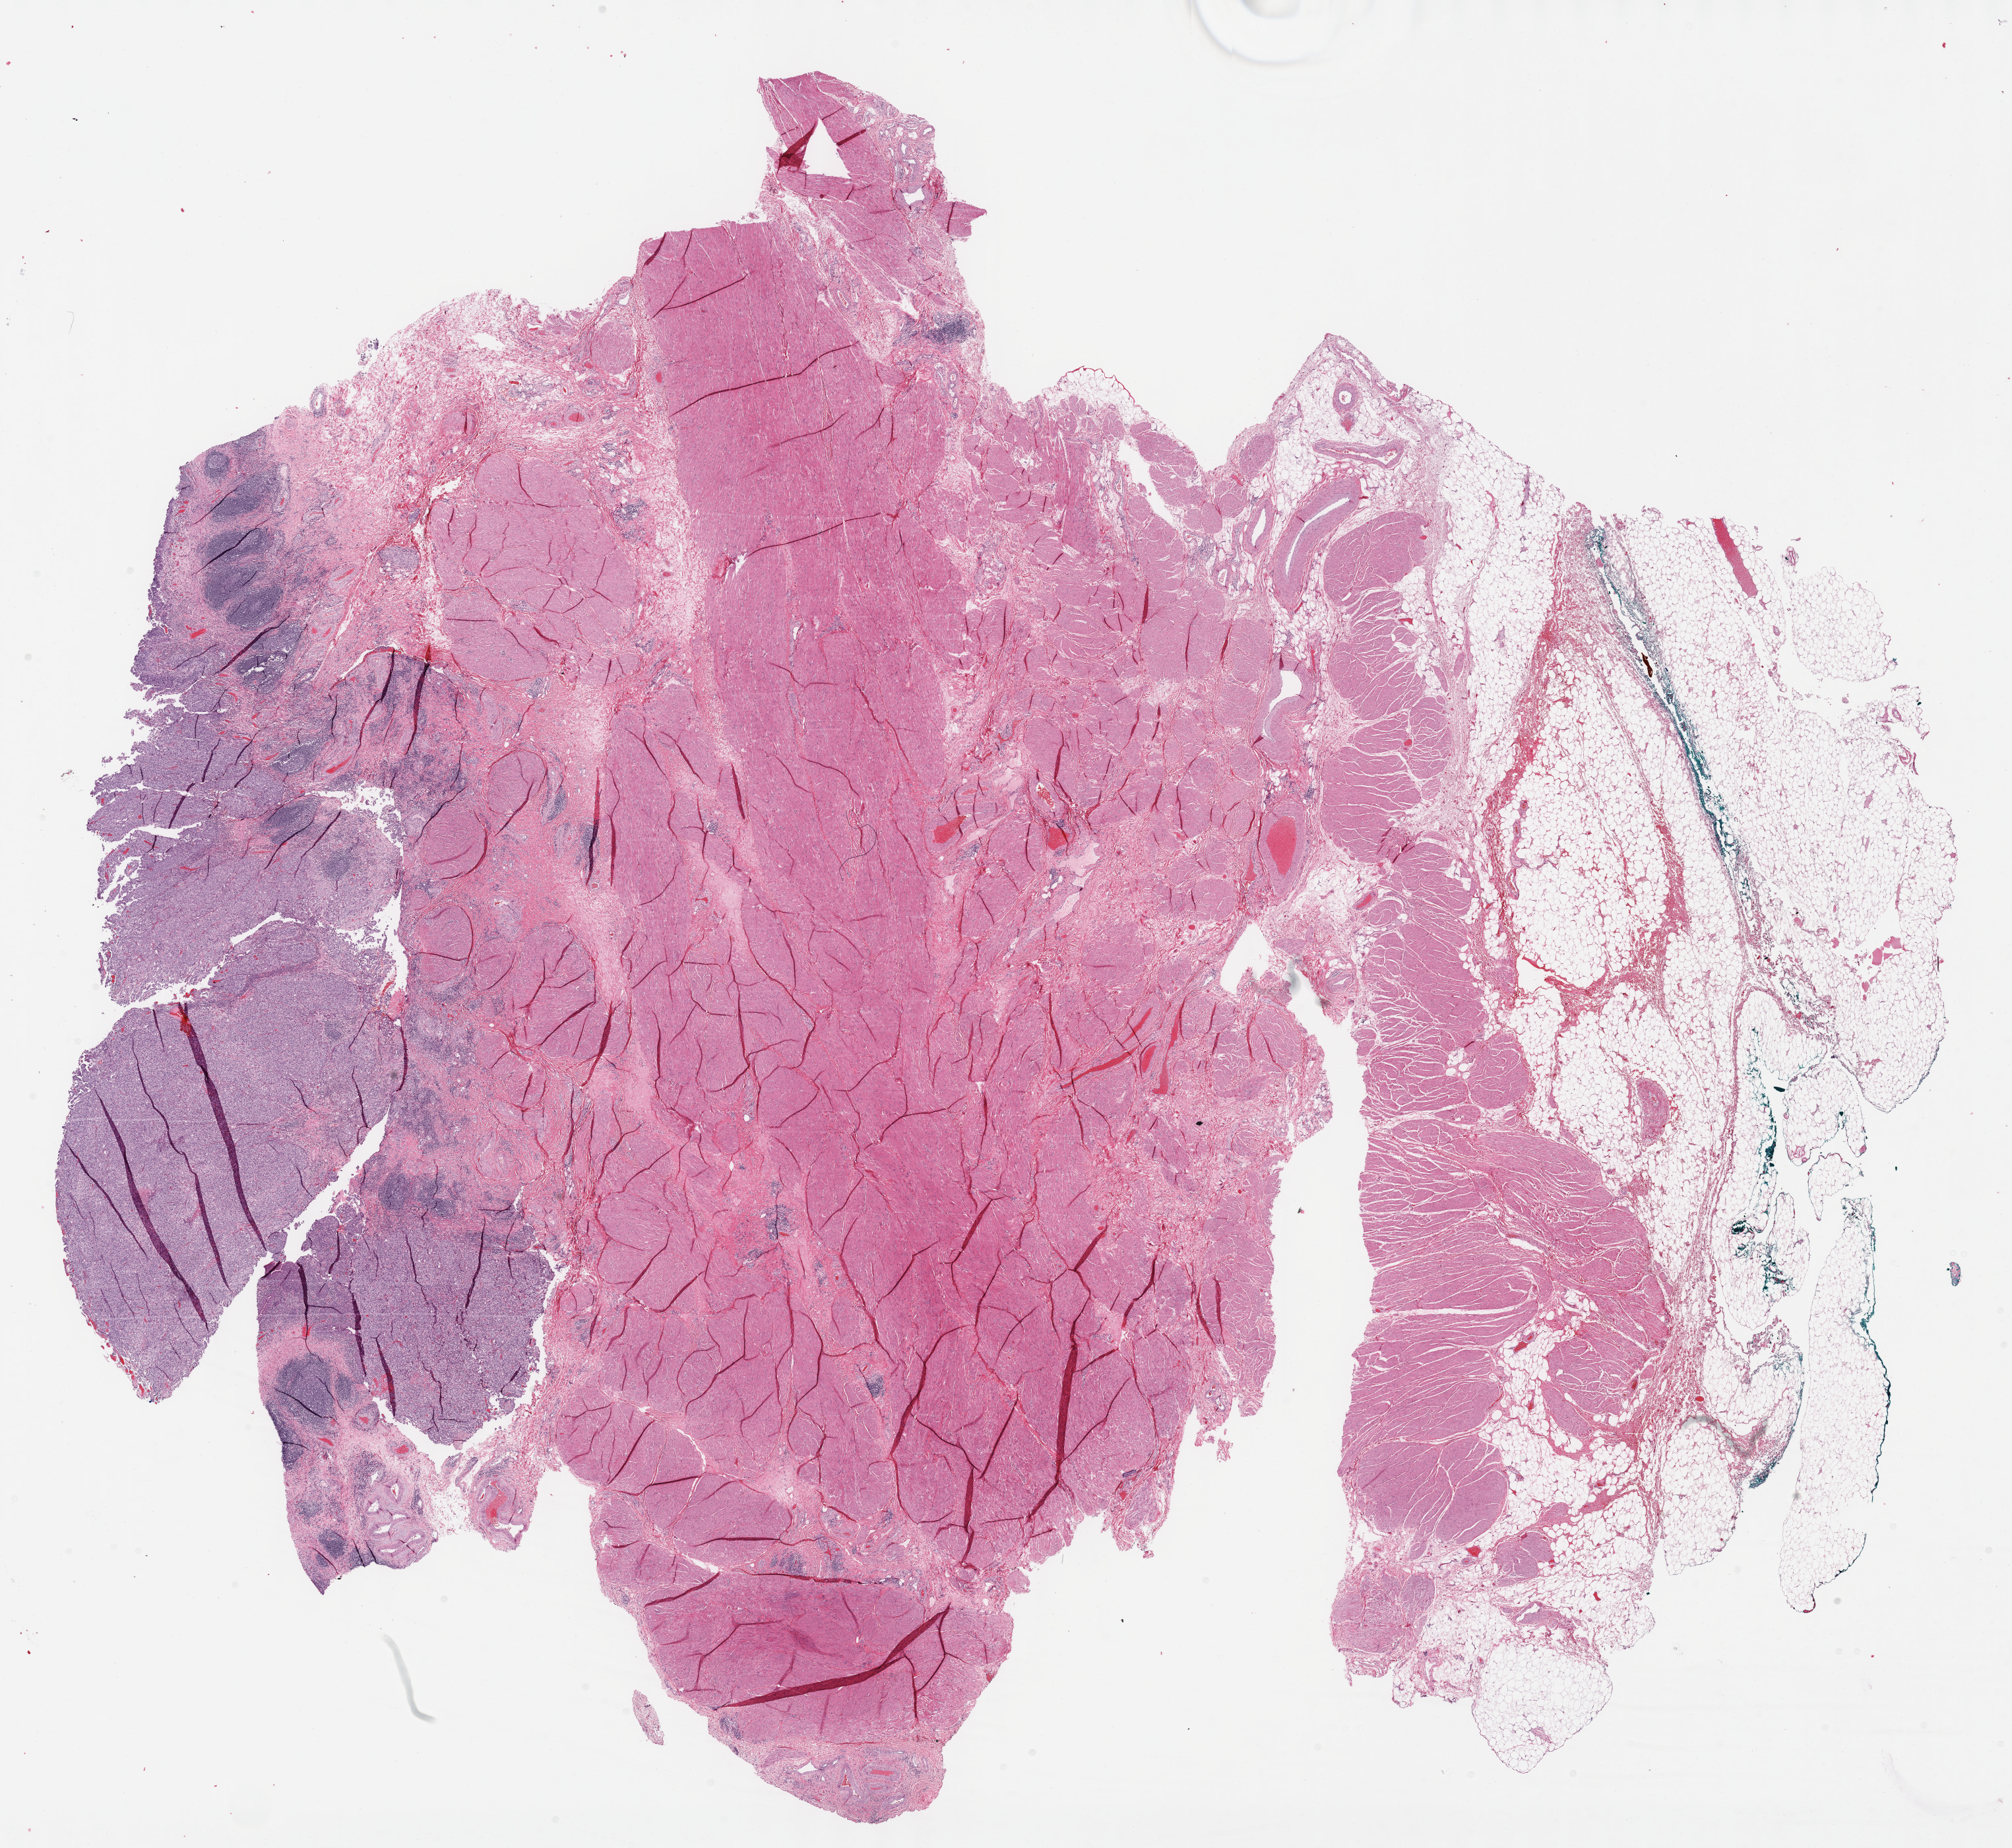
Digitized H&E tissue section (whole slide) — a low-resolution overview of the entire scanned area, about 24.6 x 22.6 mm, FFPE section, sample: primary tumour, bladder. Male patient; age at initial diagnosis 74 years. Histologic grade: high grade.
AJCC pathologic stage: IV (7th edition). Lymph nodes positive (case pathology): 2 of 12 examined. Pathologic diagnosis: Transitional cell carcinoma.